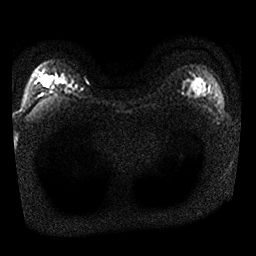
Breast MRI, one axial slice. Slice 22 of 25 in the series (ordered by position). Diffusion-weighted series; image 2 of 4 stored at this slice position (different b-values; order by instance number). 1.5 T. 4 mm slice thickness. 256 × 256 image matrix. Female patient.
Outlined on this slice (manually delineated by an expert):
- tumour on diffusion-weighted imaging: bounding box (x1, y1, x2, y2) in pixels: (42, 76, 49, 87)